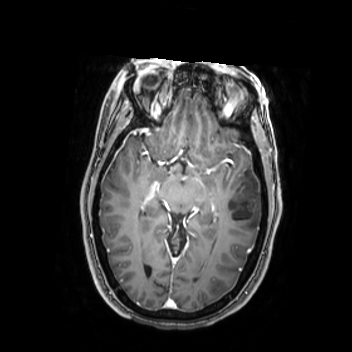
Brain MRI from a brain-tumour surgery series, one axial slice. Position 152 of 350 along the scan axis. T1-weighted post-contrast. 0.9 mm slice thickness. 352 × 352 image matrix. From the clinical record (not read from this slice): histopathology: Oligodendroglioma; WHO grade: 2; IDH mutation: yes; tumour location: Left Middle Temporal Gyrus.
Annotated regions visible in this slice (outlined manually by an expert reader):
- tumour: bounding box [x1, y1, x2, y2] px = [224, 174, 262, 233]